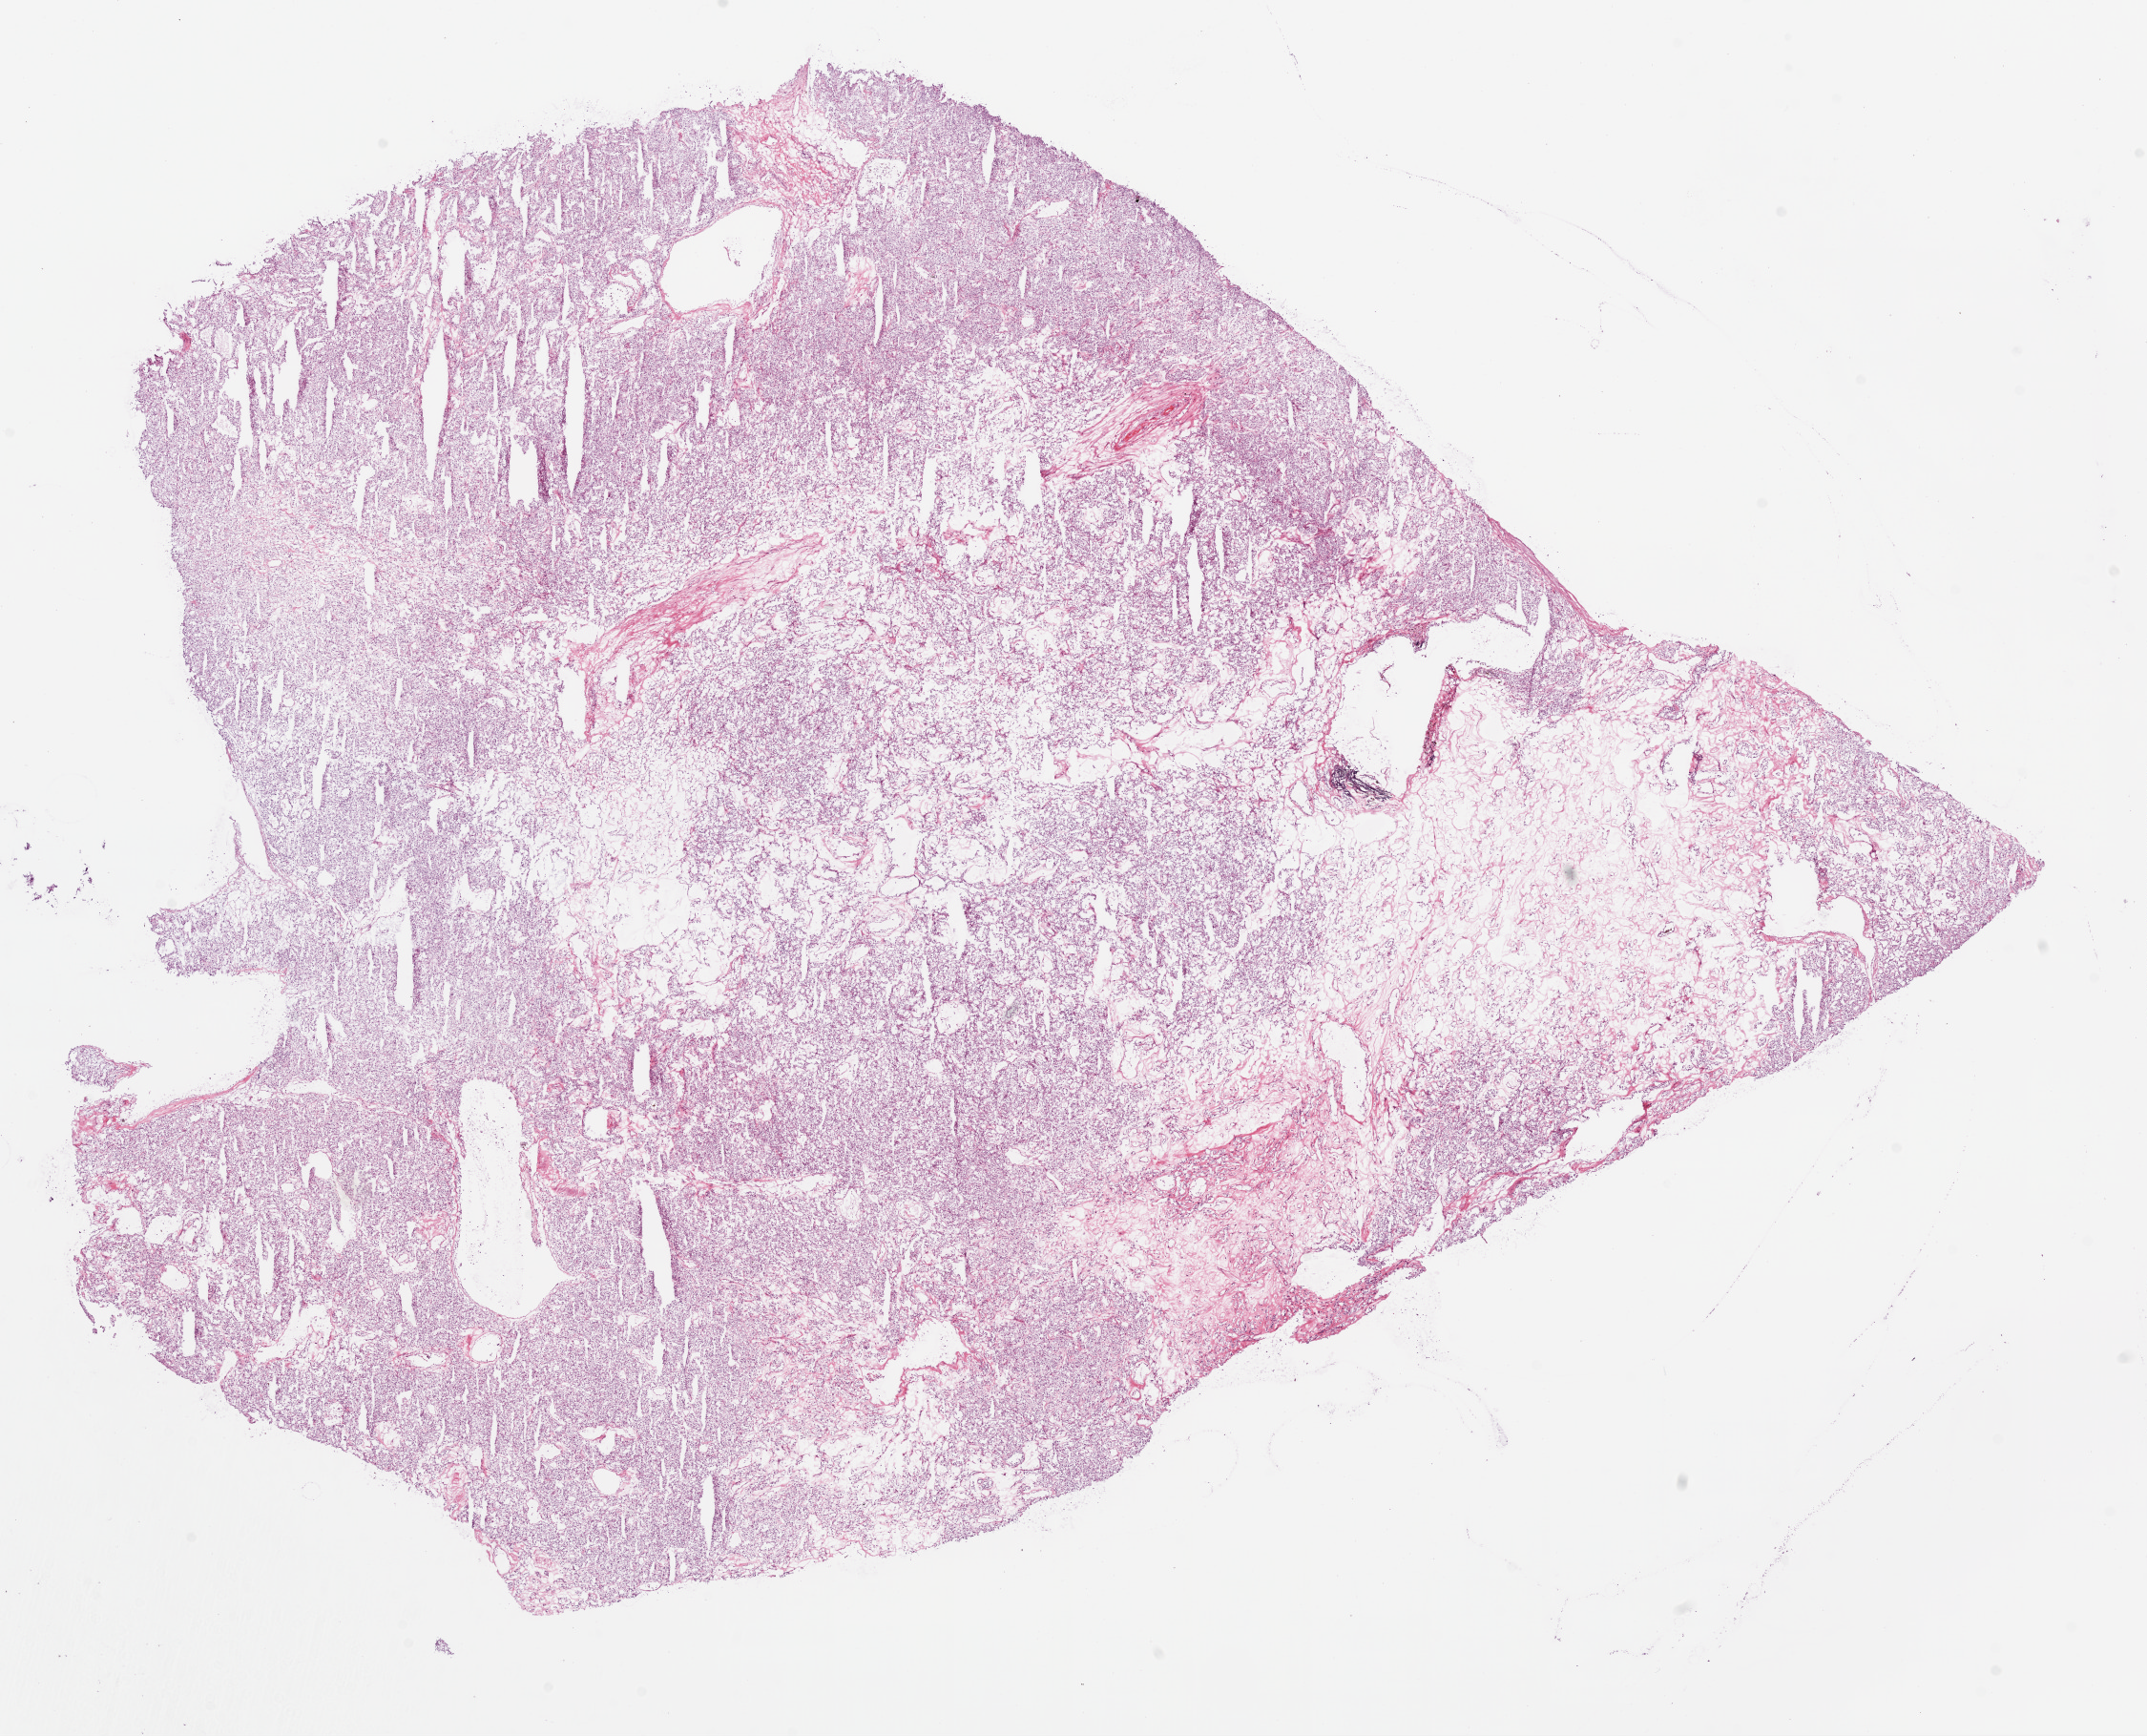
Digitized H&E-stained tissue section (whole slide) — a low-resolution overview of the entire scanned area, about 18.1 x 14.6 mm, frozen section, primary tumour sample from the kidney. Patient: male, age at initial diagnosis 64 years.
Diagnosis: Clear cell adenocarcinoma, NOS.